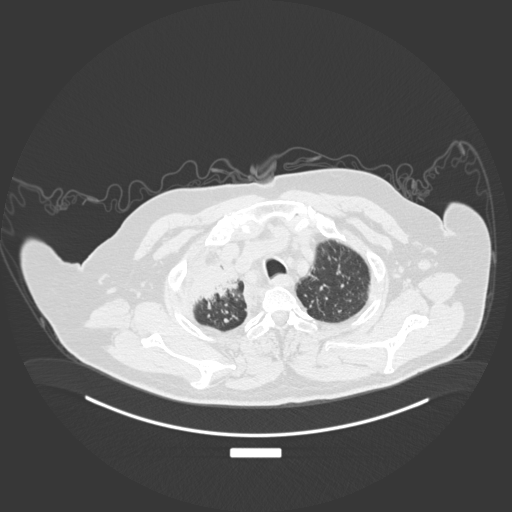
Chest CT, one axial slice. Position 166 of 201 along the scan axis. Lung window (W 1500 / L -600 HU). 1 mm slice thickness. 512 × 512 image matrix, field of view 500 × 500 mm. Patient: male, 69 years. From the clinical record (not read from this slice): clinical TNM (as recorded): T4 N3 M1.
Annotated regions visible in this slice (rectangle marked by the reading radiologist):
- lung tumour (recorded histology: adenocarcinoma): bounding box (x1, y1, x2, y2) in pixels: (184, 256, 240, 307)